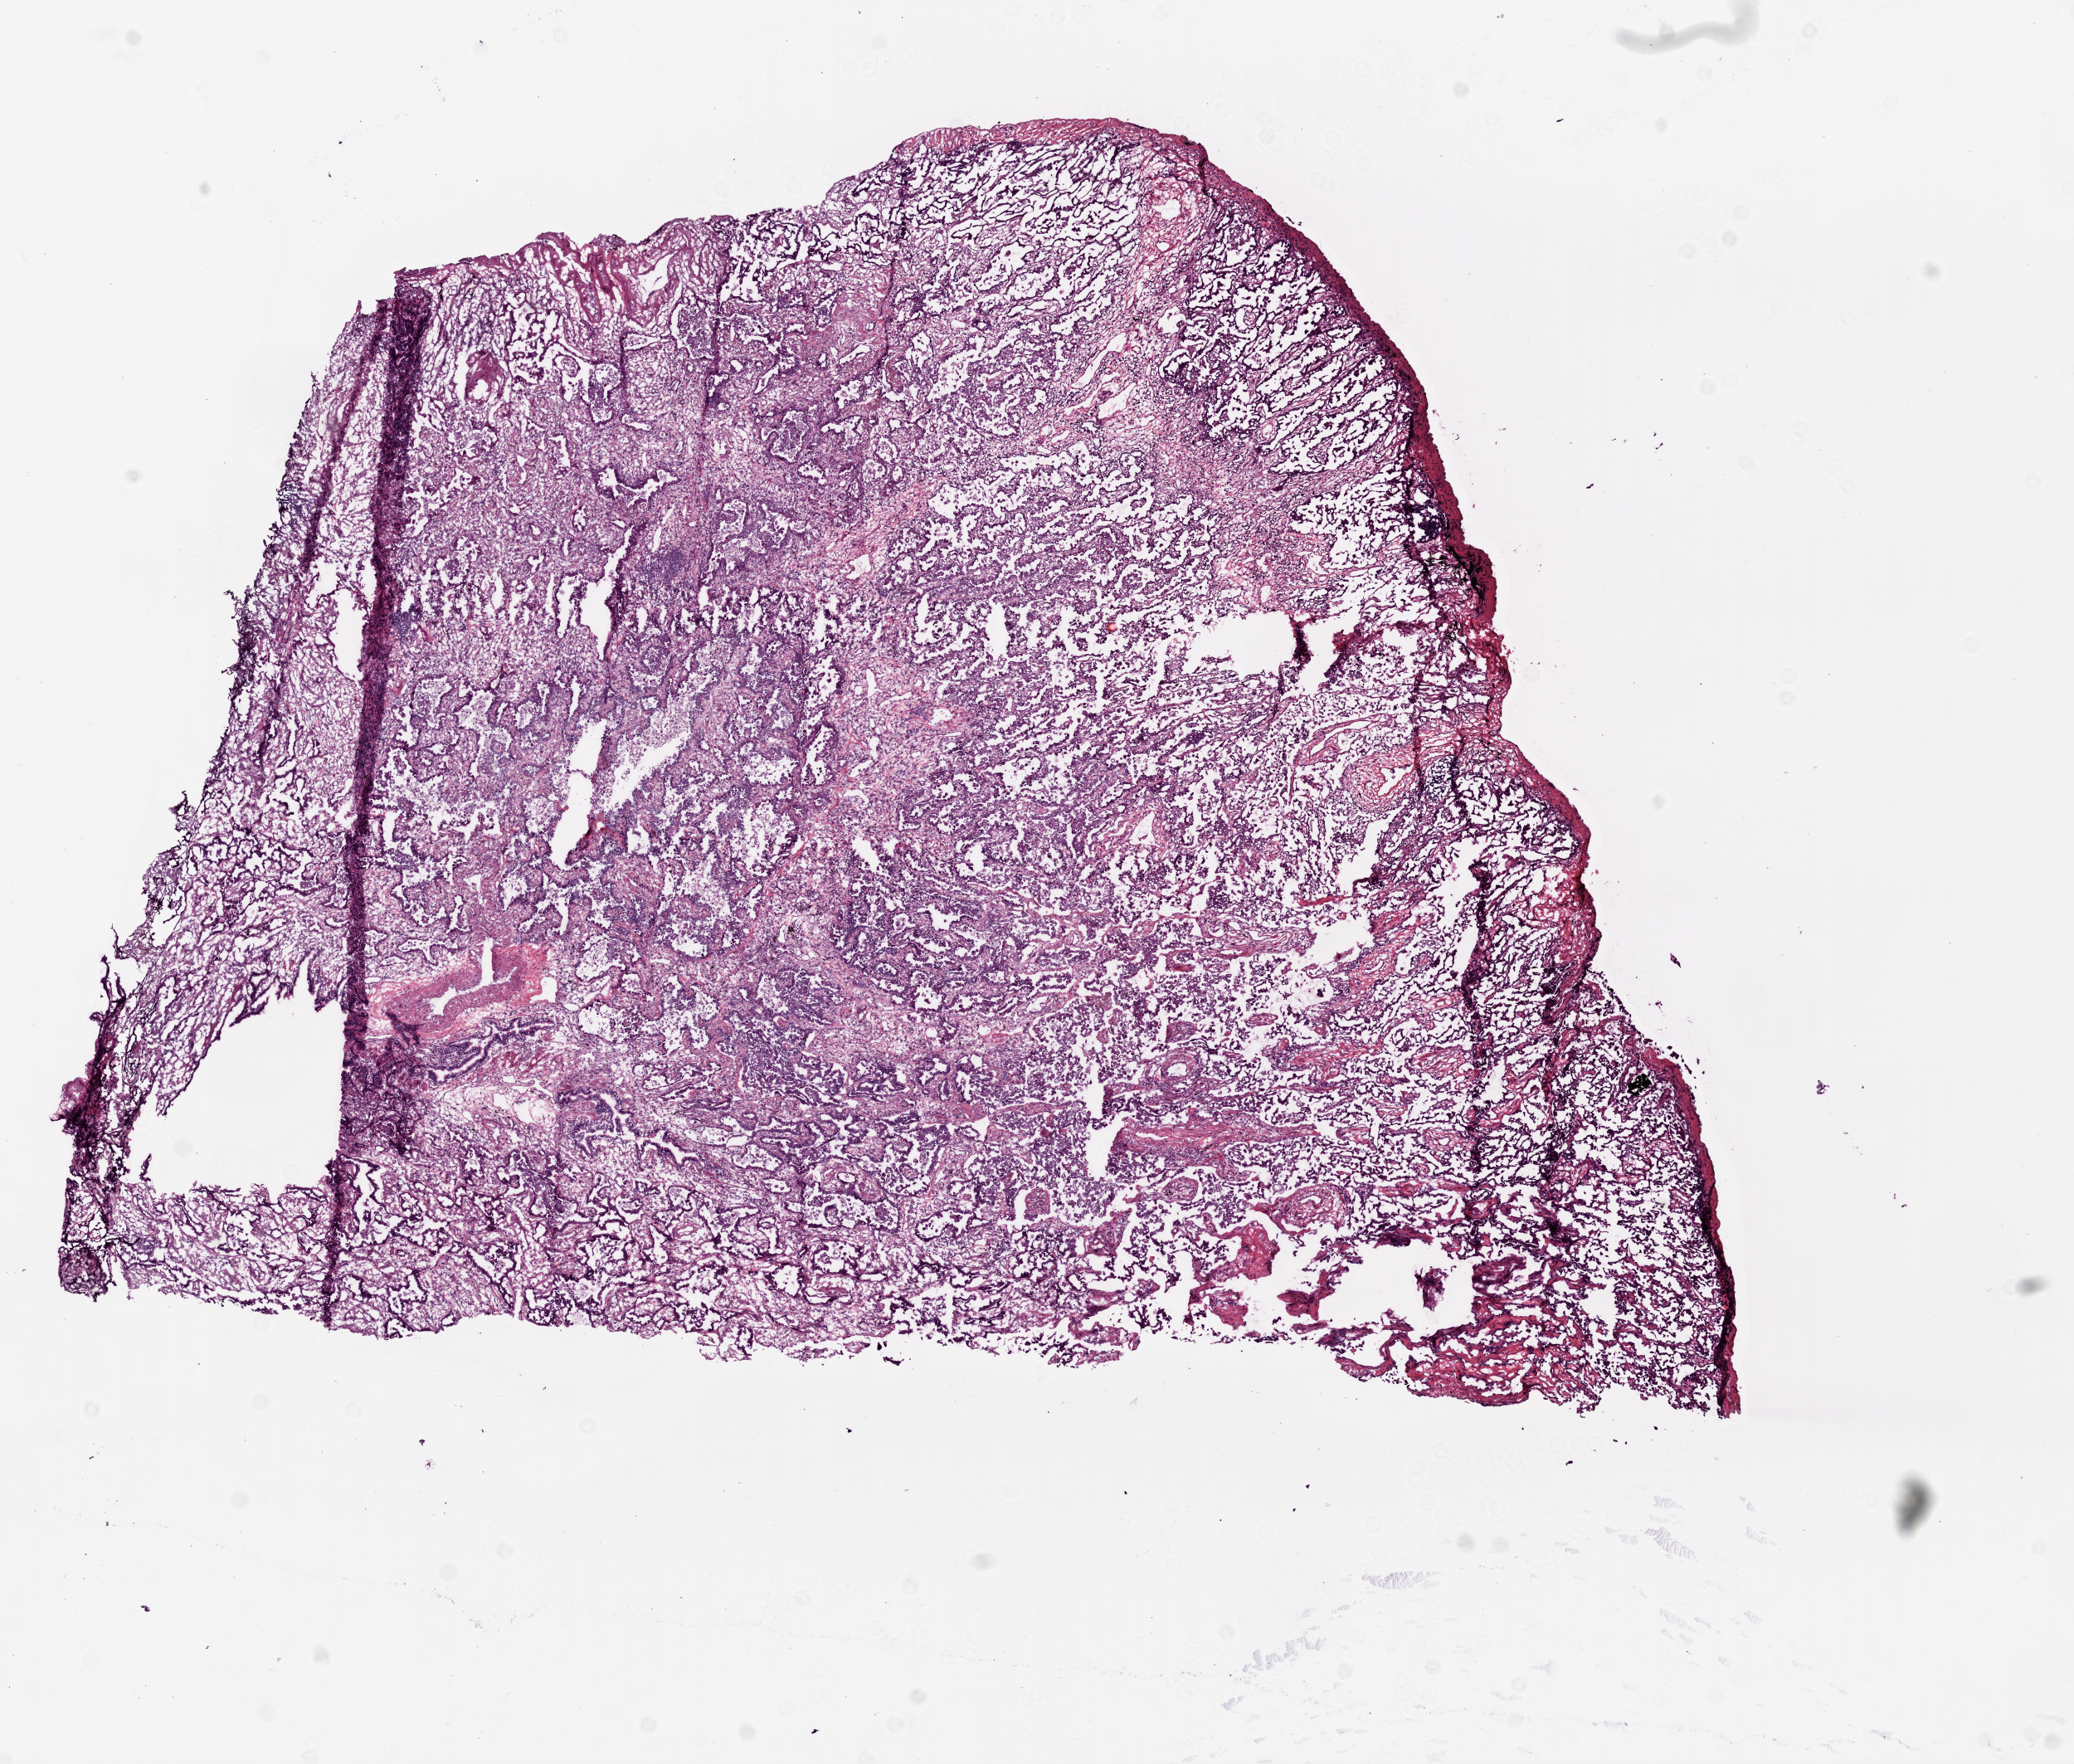
Whole-slide histology image, H&E-stained, a low-resolution overview of the entire scanned area, about 10.0 x 8.5 mm. Frozen section from the bottom of the tissue portion. Sample: primary tumour, lung. Female patient; age at initial diagnosis 61 years. Slide review estimates, as recorded: tumour cells 85%, tumour nuclei 75%, normal cells 0%, stromal cells 15%, necrosis 0%.
Diagnosis: Adenocarcinoma, NOS (lower lobe, lung). AJCC pathologic stage: IIB (4th edition).